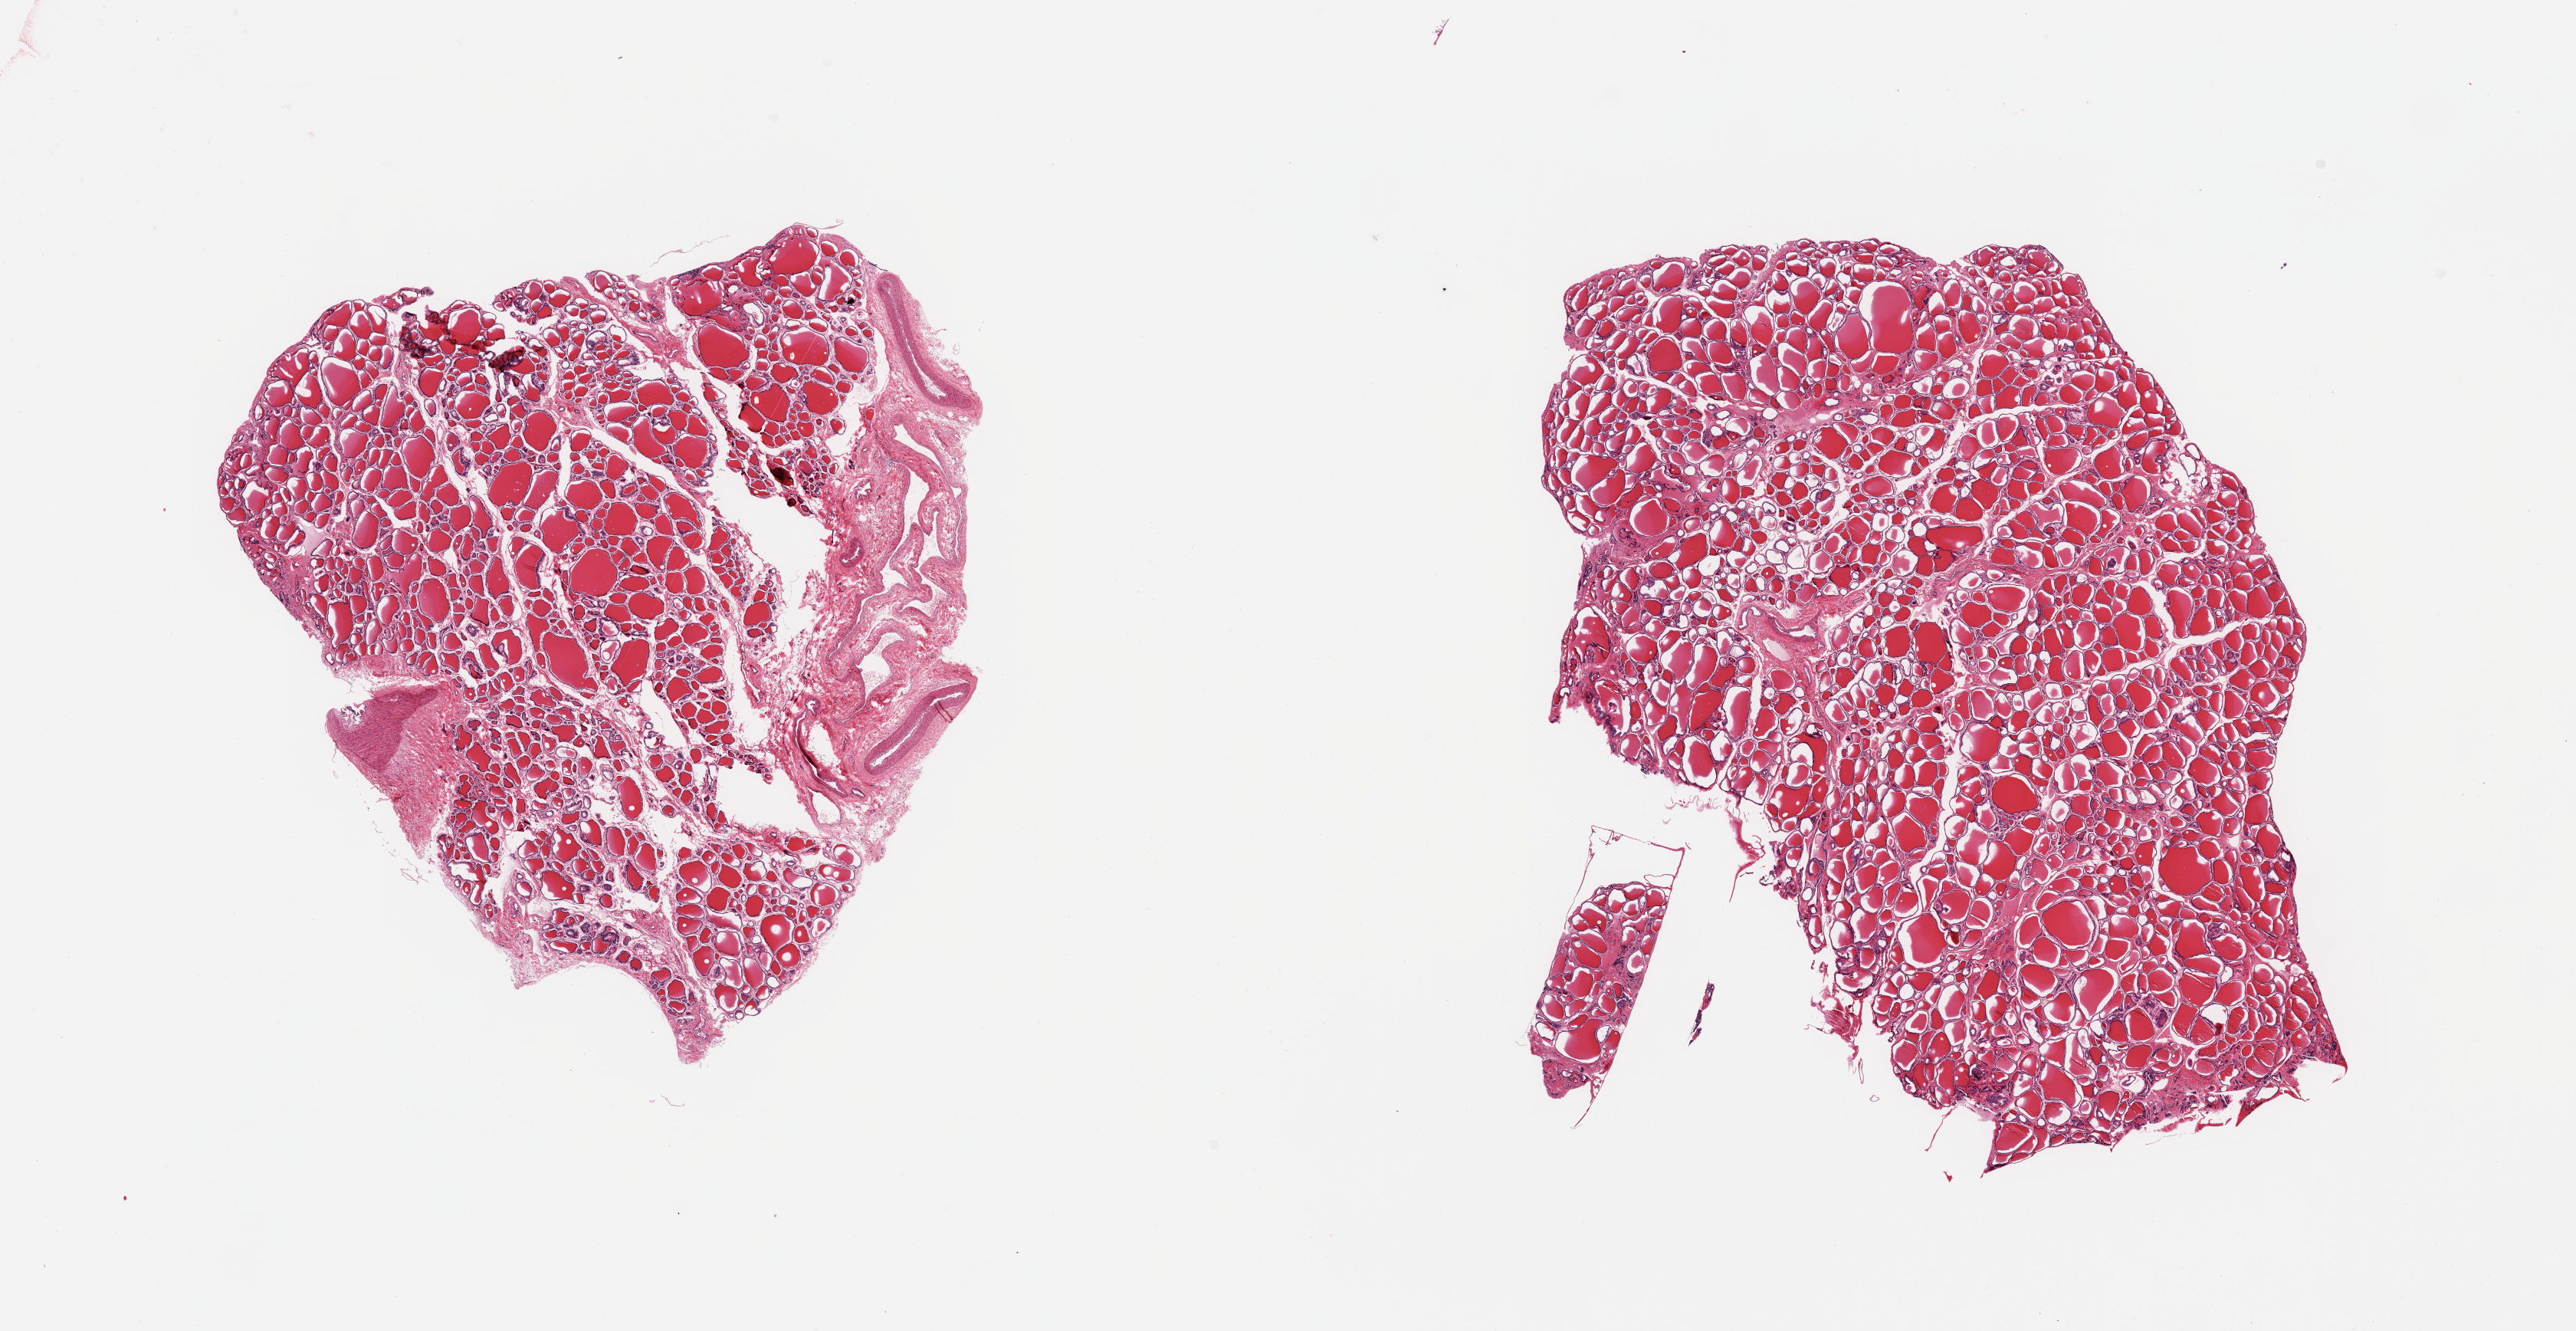
Whole-slide image, haematoxylin and eosin stain, brightfield, whole scanned area (about 26.6 x 13.7 mm, acquisition: 20x scan) shown as a low-resolution overview; PAXgene-fixed paraffin-embedded (PFPE) section; section of thyroid (target tissue); donor tissue sample. Donor: male.
- review note (as recorded): 2 pieces, ~5 x1.5 adherent nubbin of perithyroidal fibrovascular tissue; Floater in block, tagged